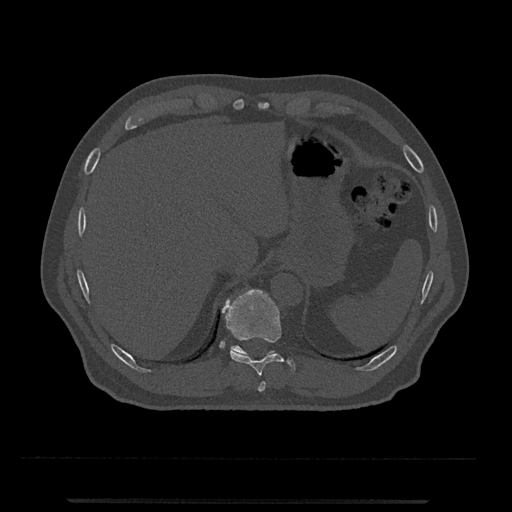
CT including the spine, one axial slice; slice 507 of 797 in the series (ordered by position); reconstruction kernel Br40s/3; 120 kVp; bone window (W 1800 / L 400 HU); 0.5 mm slice thickness; 512 × 512 image matrix, field of view 419 × 419 mm. Male patient, age 63 years. From the clinical record (not read from this slice): primary cancer: prostate.
Outlined on this slice (semi-automatically segmented with operator editing):
- T10 vertebra: bounding box [x1, y1, x2, y2] px = [222, 289, 296, 376]
- T11 vertebra: [231, 345, 275, 356]
- T9 vertebra: [258, 381, 266, 392]